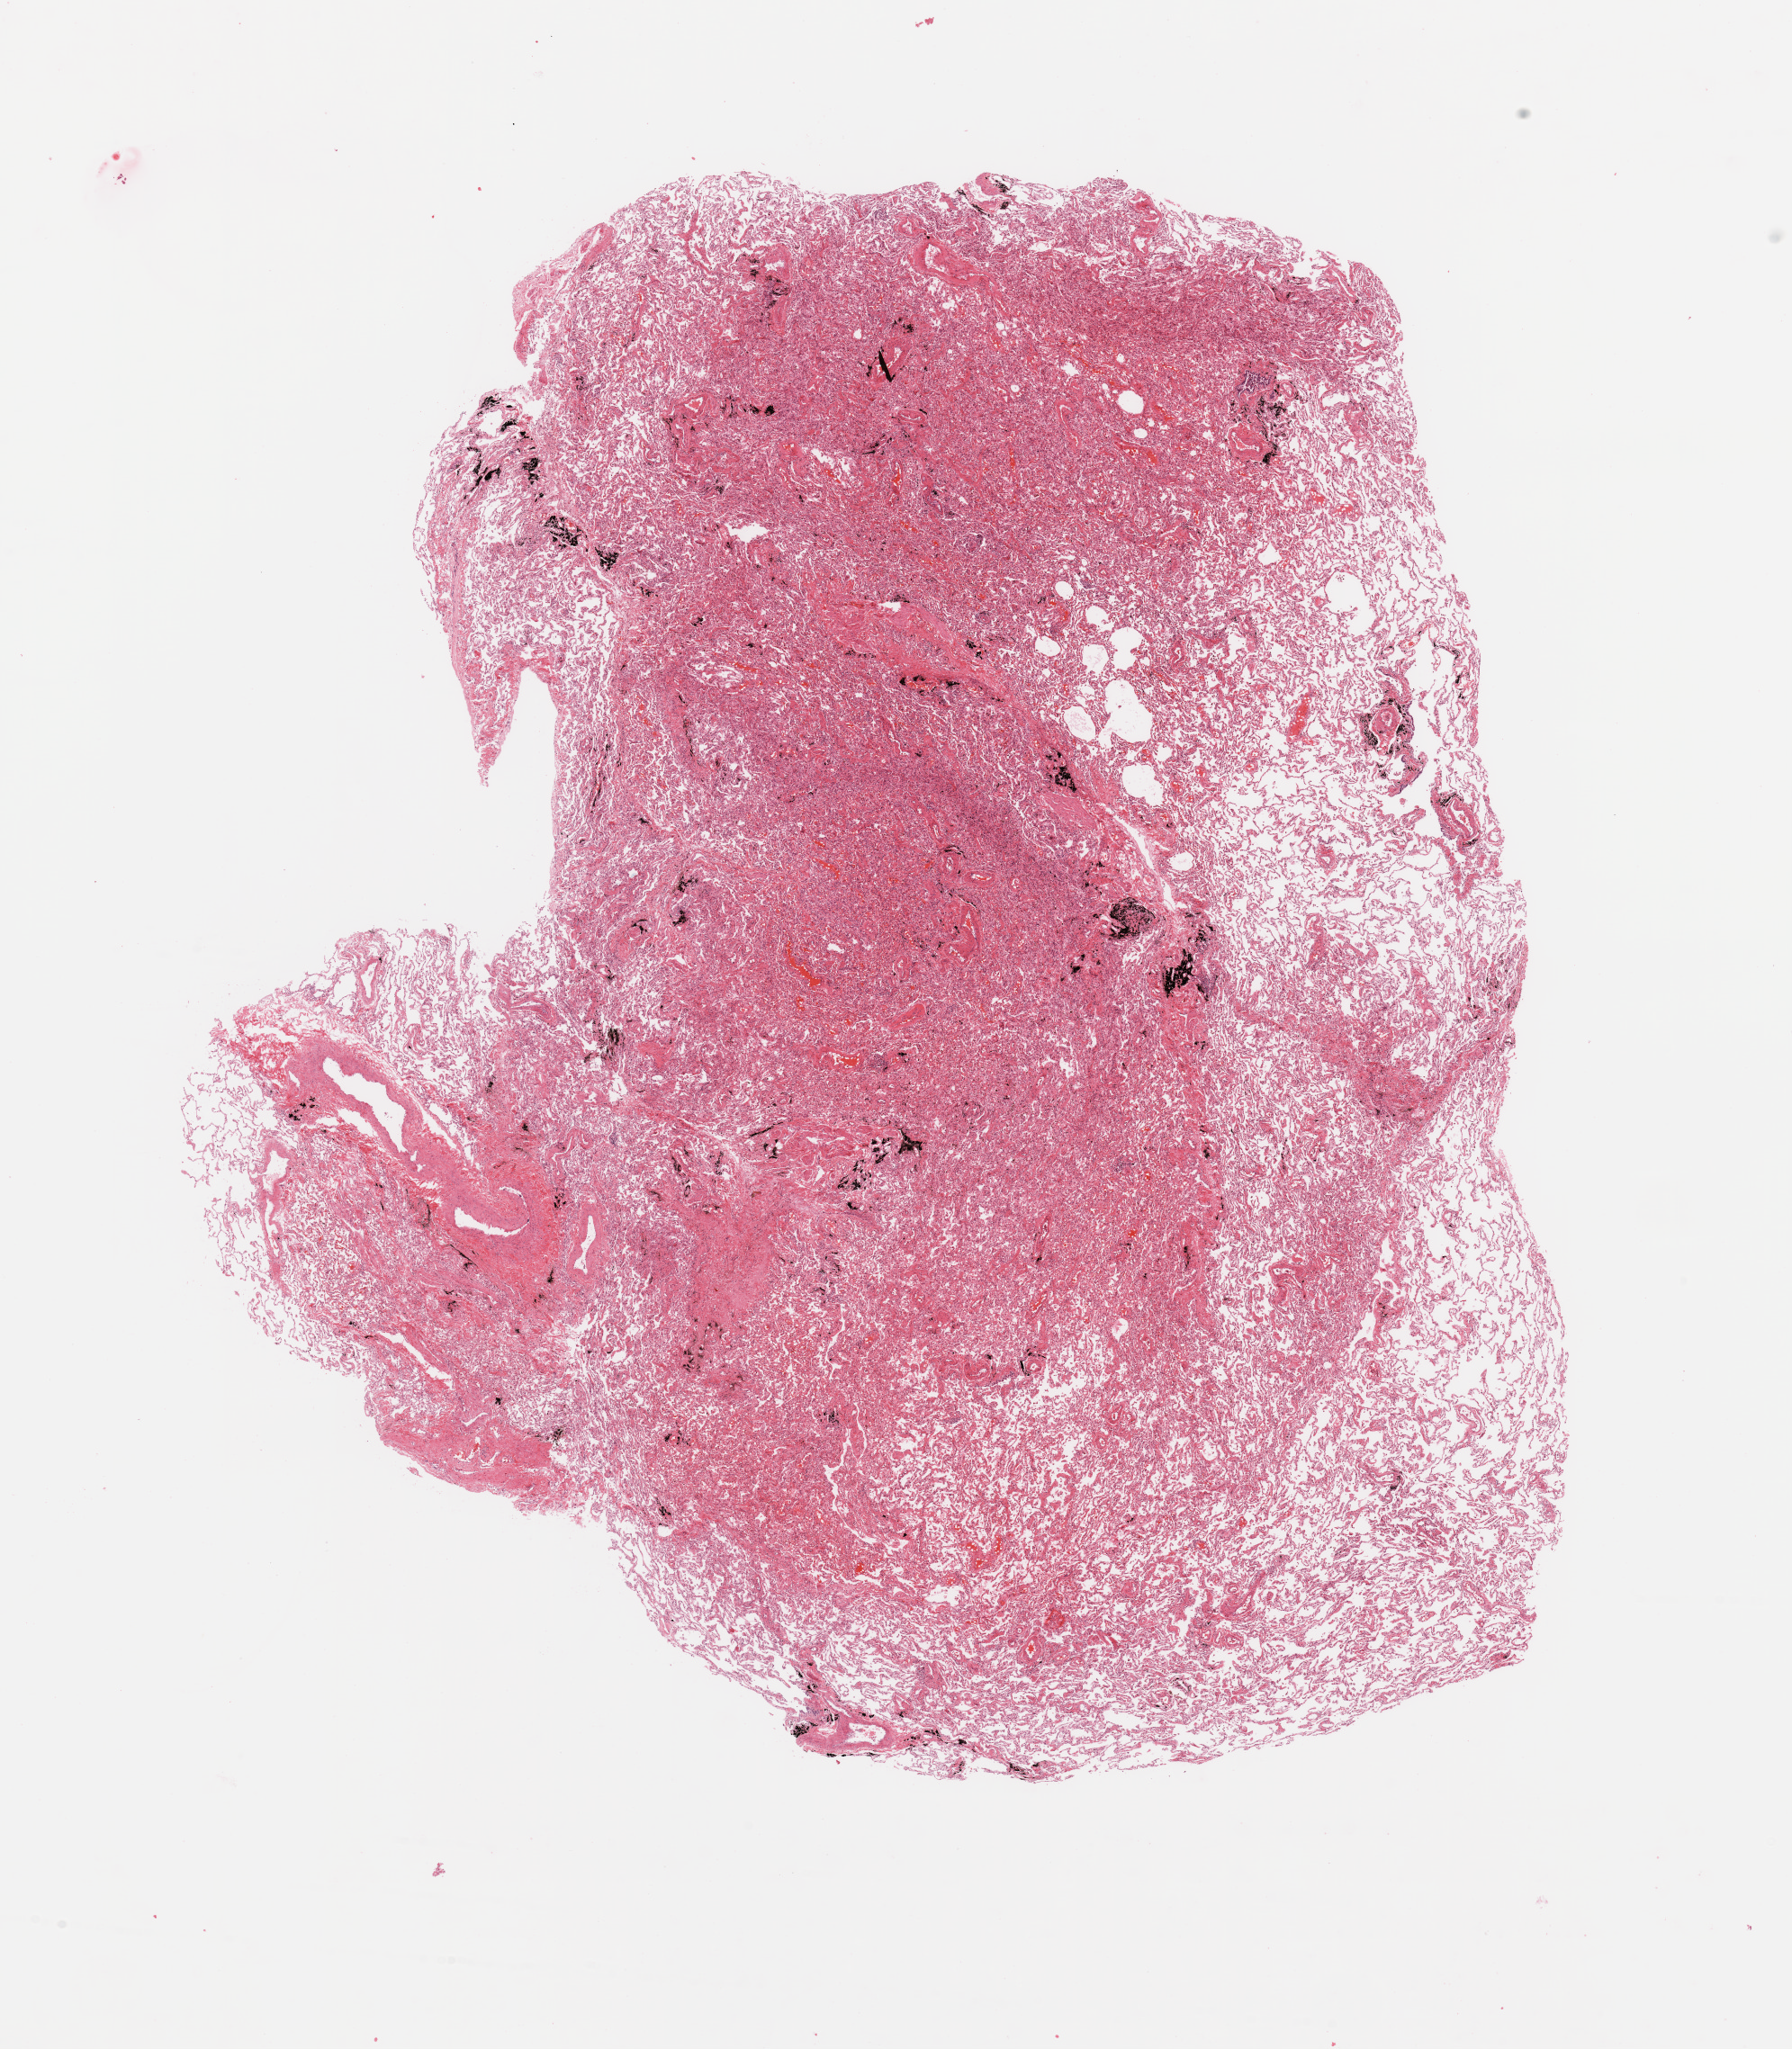
Digitized H&E tissue section (whole slide), whole scanned area (about 15.8 x 18.0 mm) shown as a low-resolution overview, lung, normal (non-tumour) tissue. Patient: male, age 69 years.
- this section: normal (non-tumour) tissue from the same patient
- patient diagnosis: Adenocarcinoma, NOS